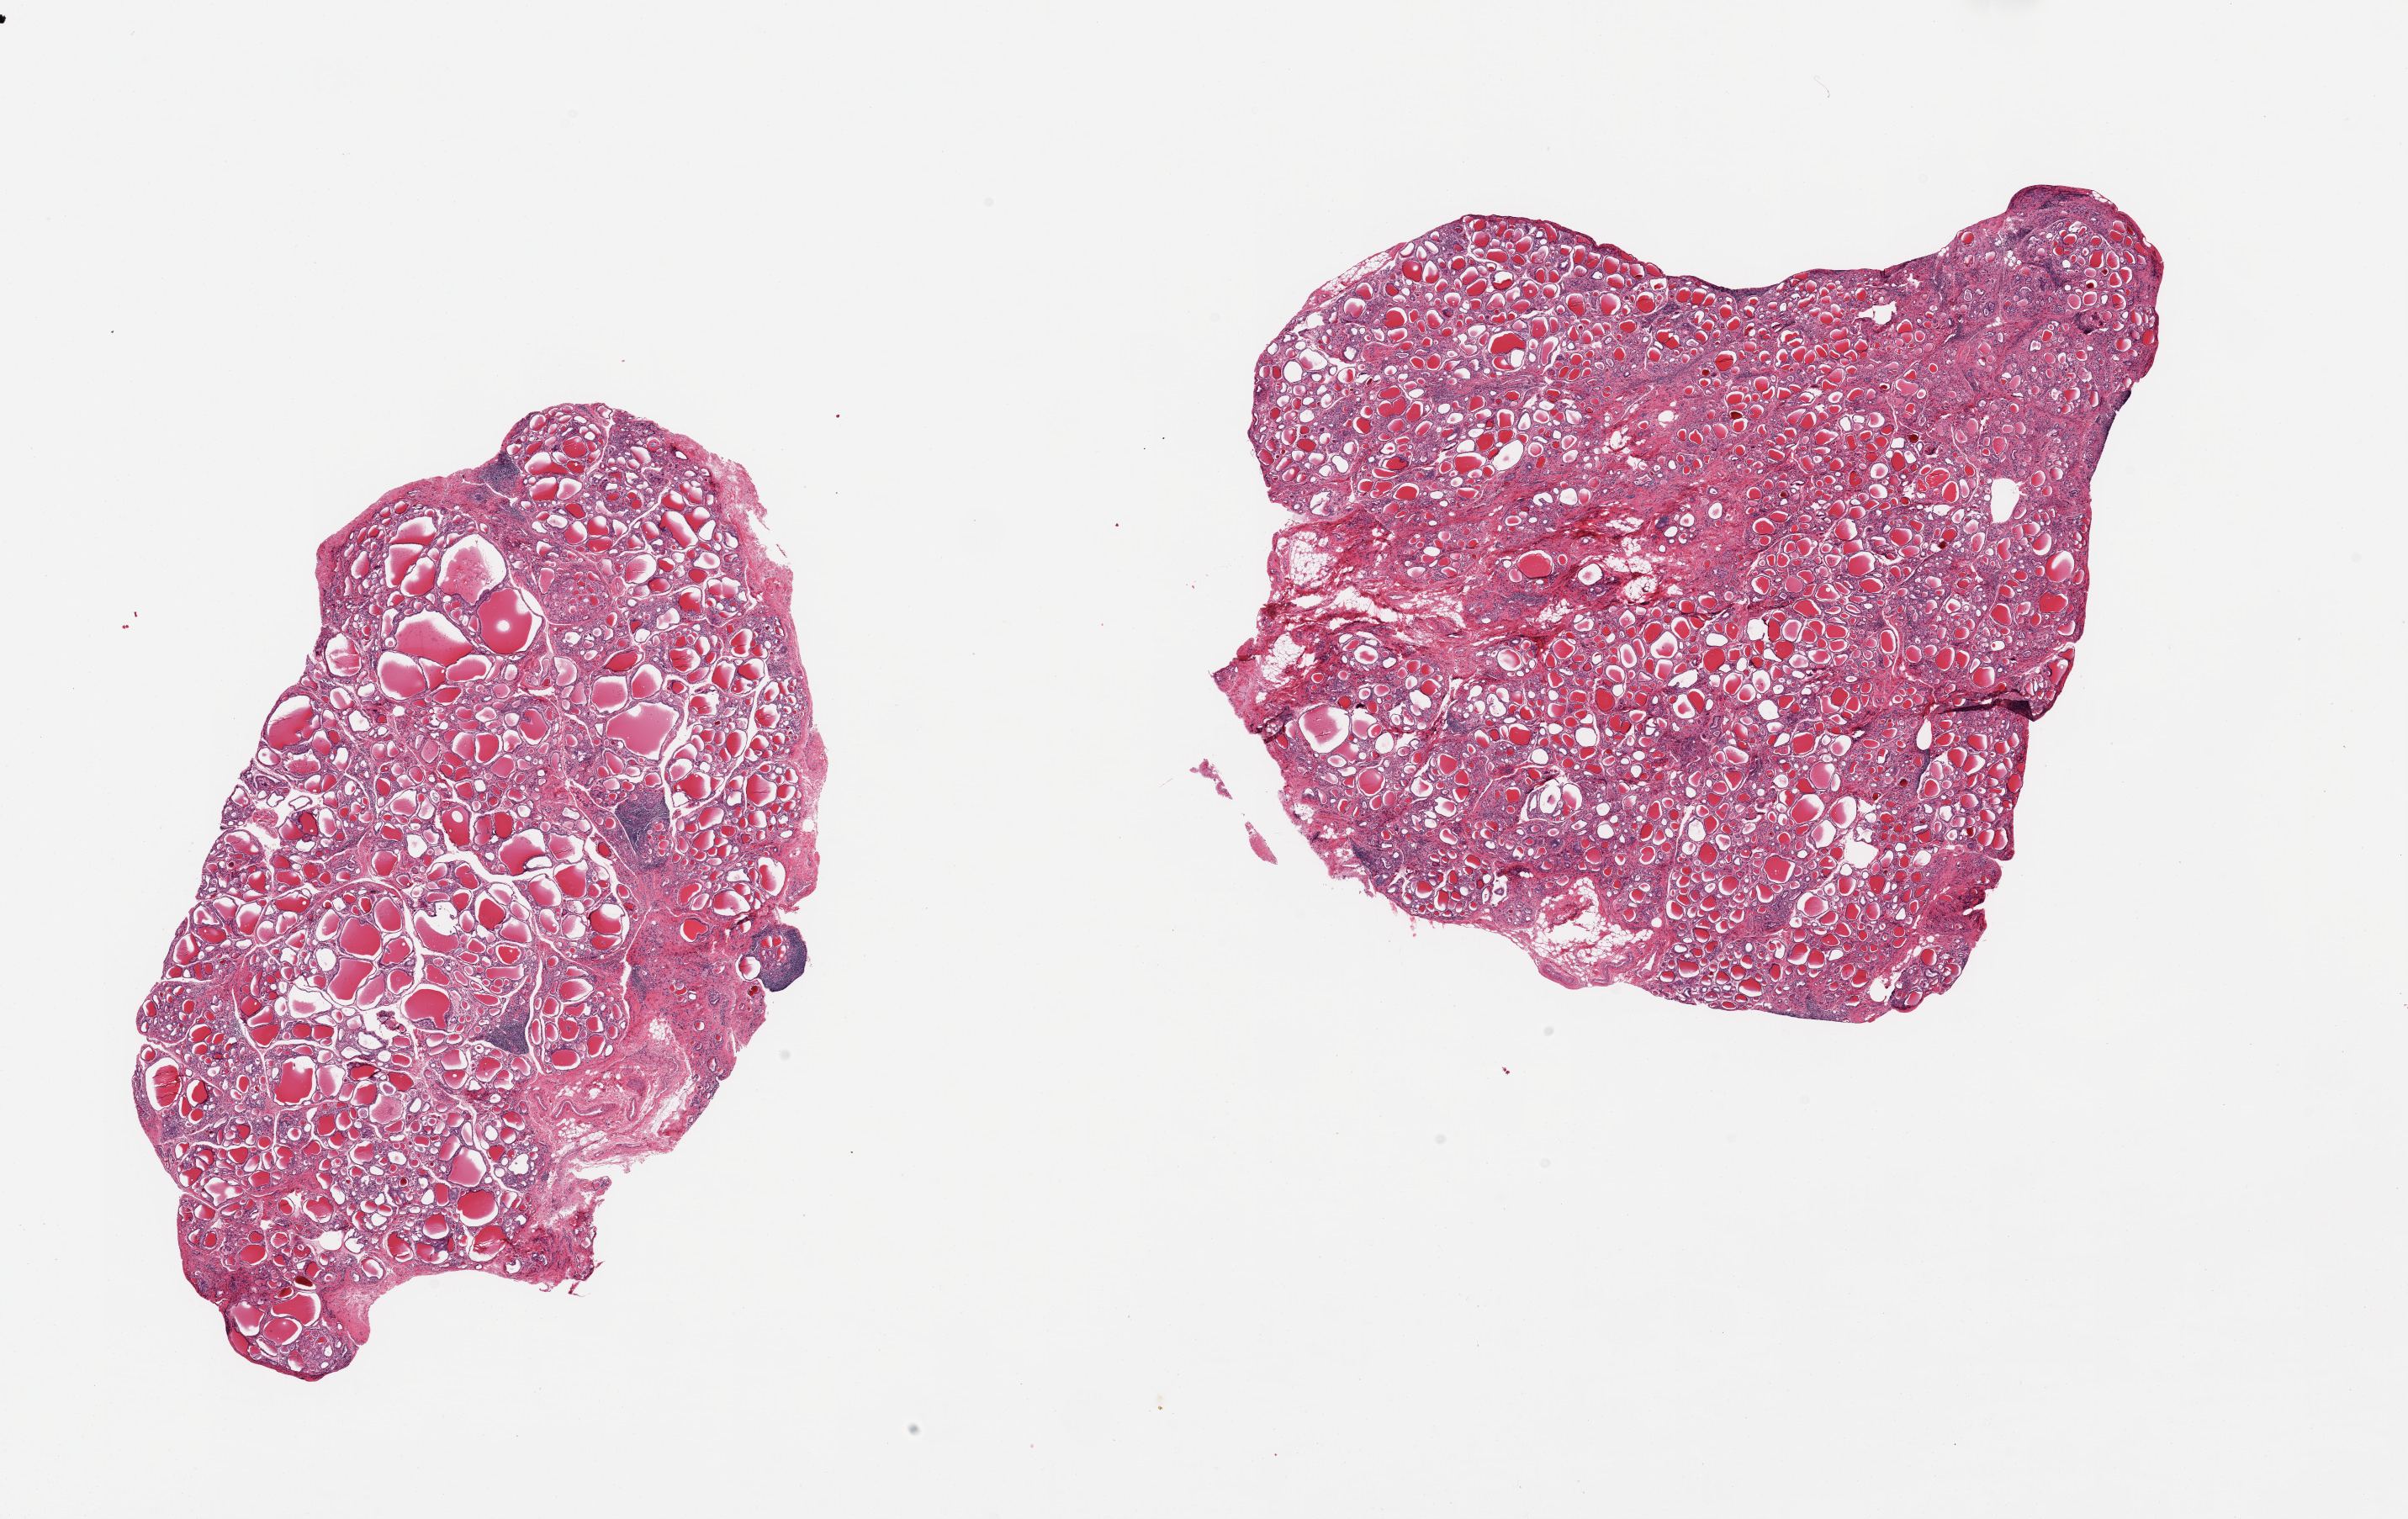
Hematoxylin and eosin (H&E) whole-slide image — whole scanned area (about 22.6 x 14.3 mm, acquisition: 20x scan) shown as a low-resolution overview. PAXgene-fixed, paraffin-embedded tissue. Section of thyroid (target tissue). Tissue donor sample. Donor sex: male.
Review note (as recorded): 2 pieces few foci of lymphocytic (Hashimoto) thyroiditis.